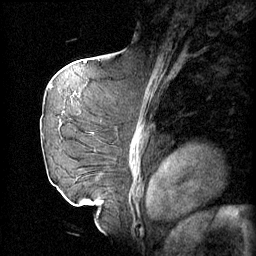
Breast MRI (dynamic contrast-enhanced), one sagittal slice. Position 39 of 60 along the scan axis. 4 images stored at this slice position (order not interpretable as contrast timing). 1.5 T. TE 4.2 ms, TR 11 ms. 2 mm slice thickness. 256 × 256 image matrix. Female patient, age 72 years.
Annotated regions visible in this slice (semi-automatically segmented with operator editing):
- analysis volume of interest (the breast-tissue region the enhancement analysis was run in; not a lesion): box from (x=47, y=68) to (x=109, y=163) px
- tumour enhancement mask (voxels above the 70 % enhancement threshold inside the analysis volume of interest): (x=53, y=68)–(x=99, y=133)